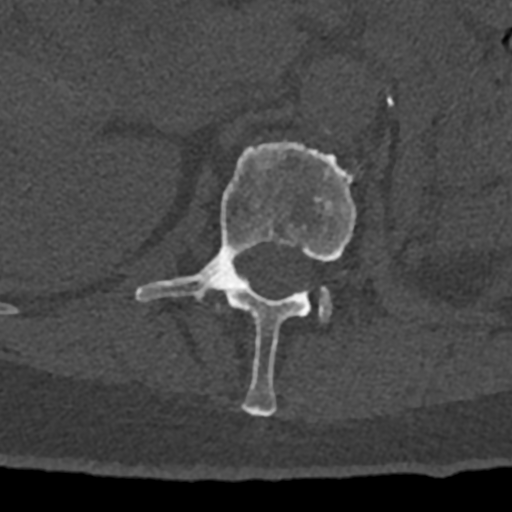
CT including the spine, one axial slice; slice 427 of 797 in the series (ordered by position); 120 kVp; bone window (W 1800 / L 400 HU); 0.5 mm slice thickness; 512 × 512 image matrix, field of view 160 × 160 mm. Patient: male, 74 years. Case-level facts recorded for this patient, not image findings: primary cancer: renal.
Structures marked on this image (semi-automatic segmentation, software-assisted and operator-edited):
- L1 vertebra: bounding box [x1, y1, x2, y2] px = [135, 140, 356, 416]
- L2 vertebra: [318, 293, 331, 322]